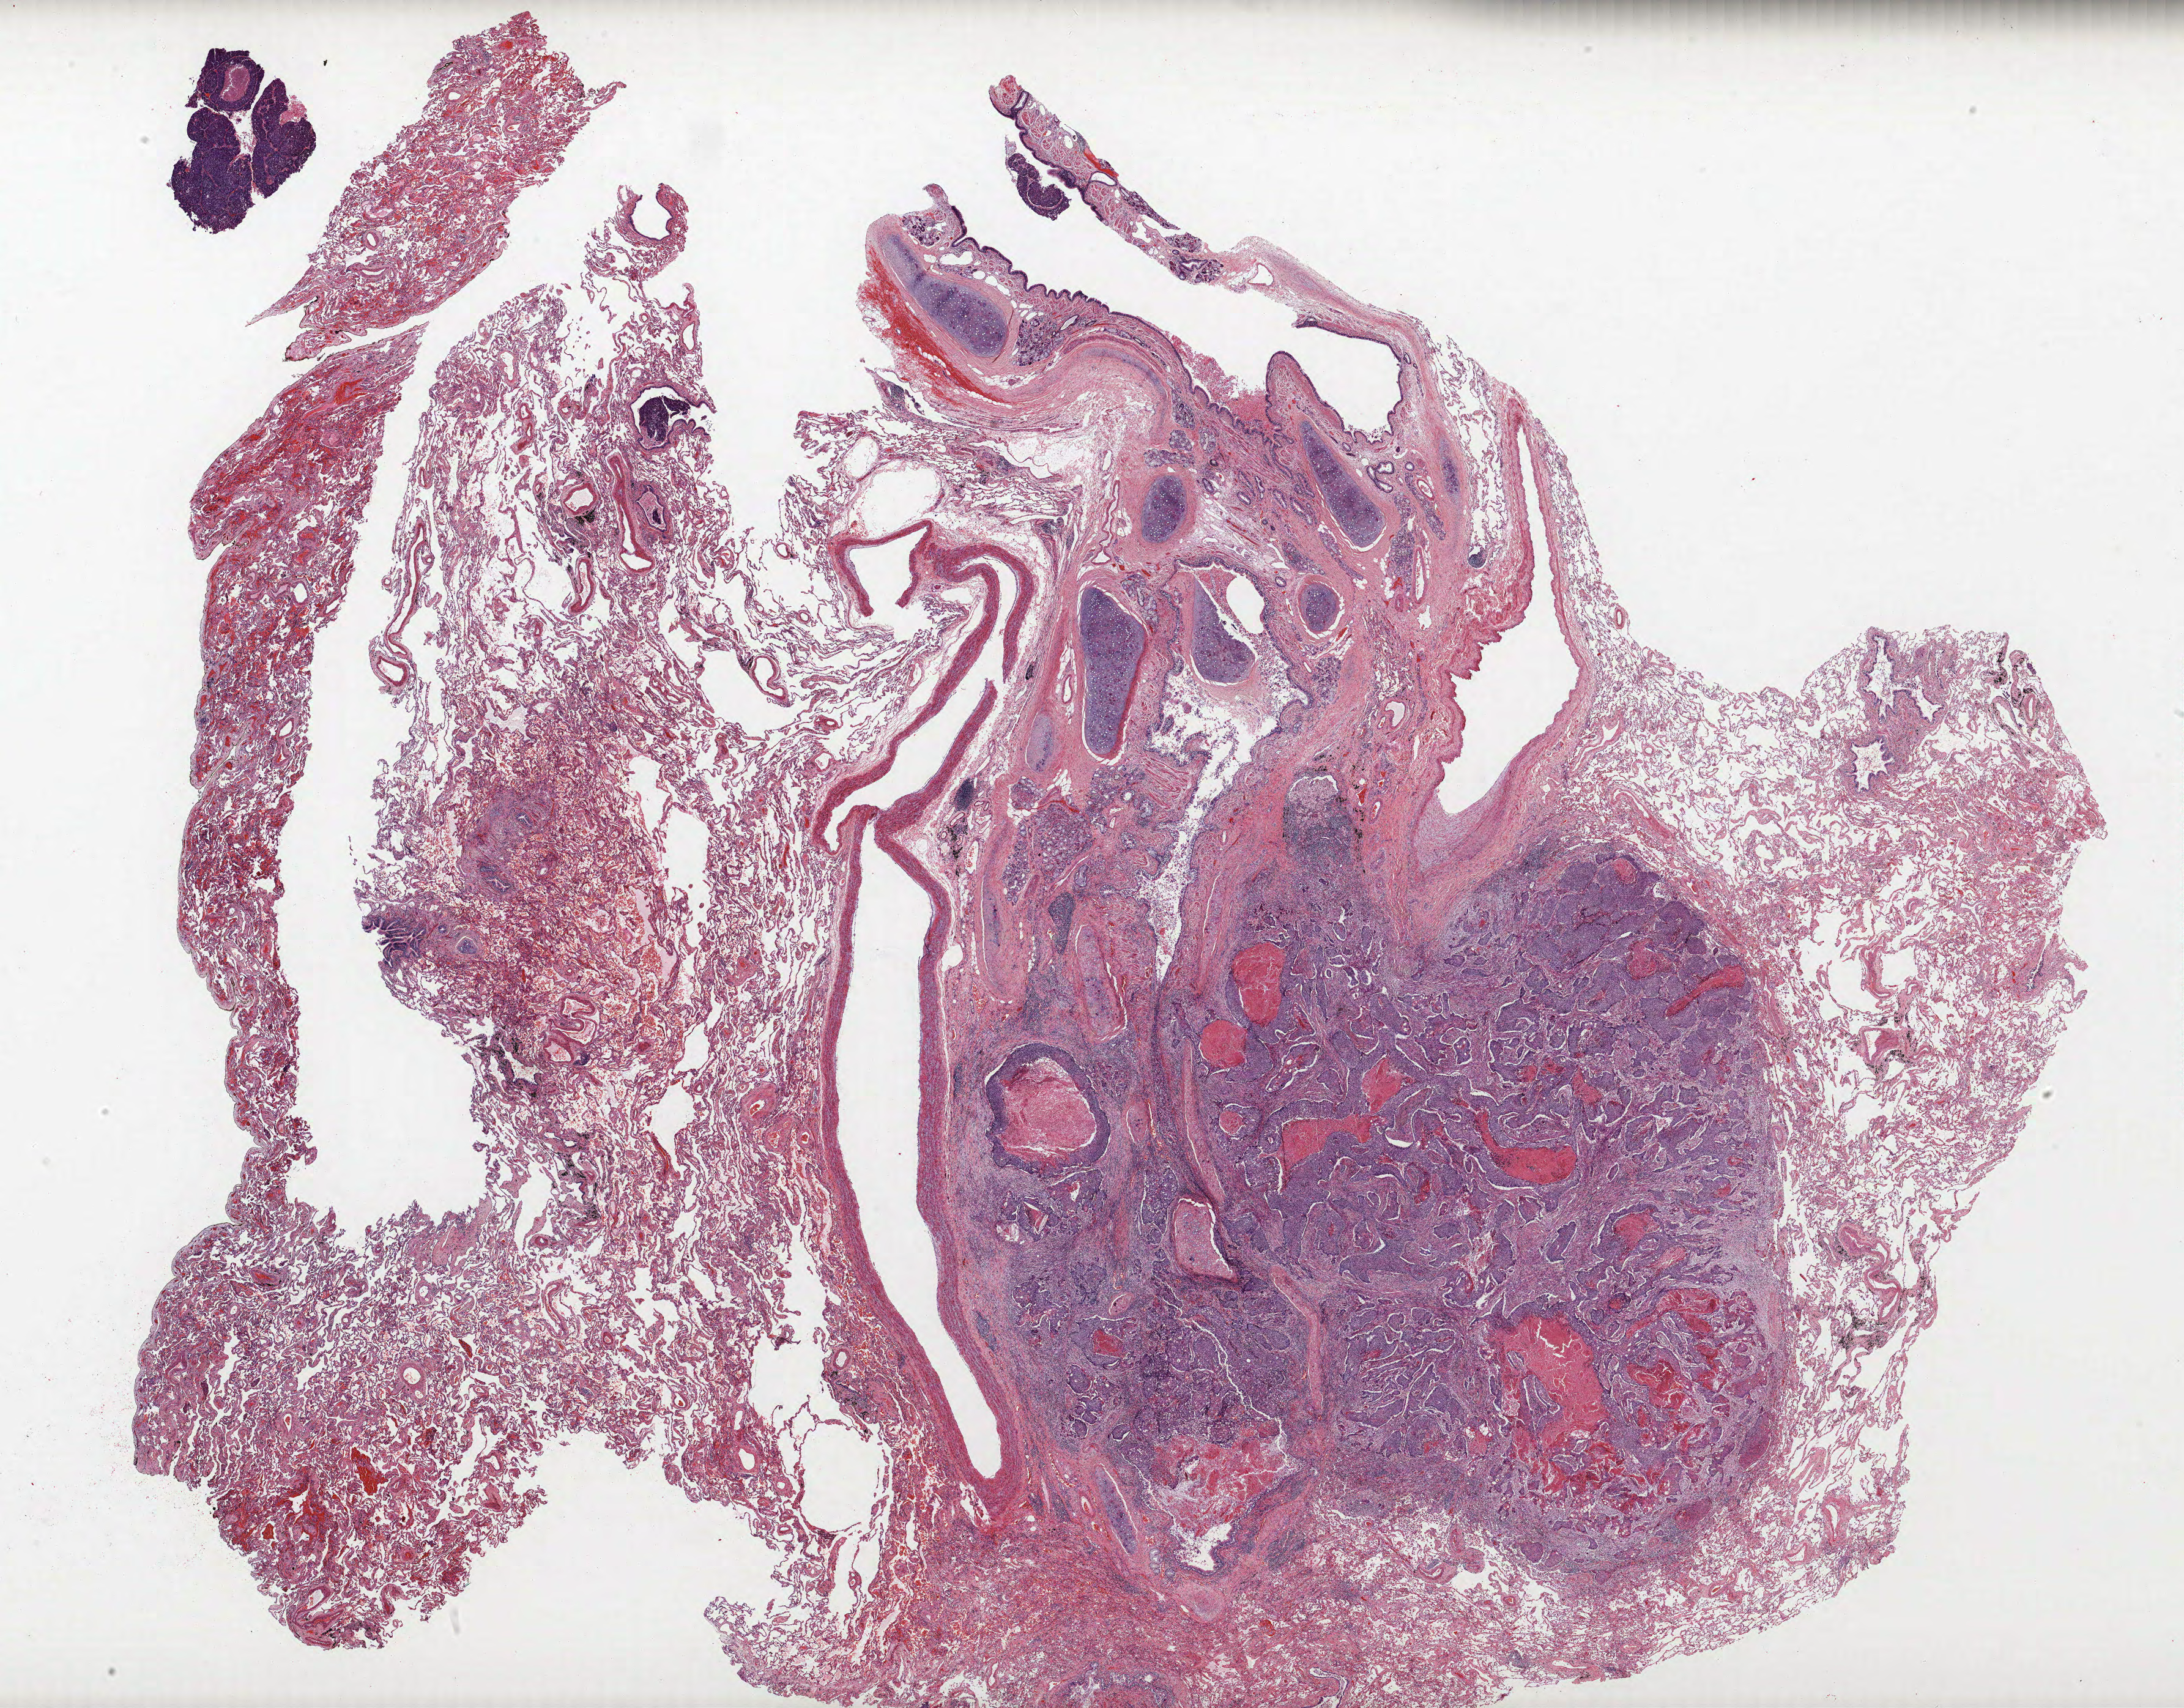
H&E whole-slide image, low-resolution overview of the scanned area, about 28.6 x 22.3 mm (slide scanned at 40x), formalin-fixed paraffin-embedded (FFPE) section, lung. Female patient, aged 65 at enrolment. Former smoker at enrolment. Grade: poorly differentiated (G3).
Participant's lung-cancer diagnosis: Squamous cell carcinoma, NOS. Primary tumour location (clinical record): right upper lobe. Stage (AJCC 6th edition): IB. Tumour size (pathology): 35 mm.